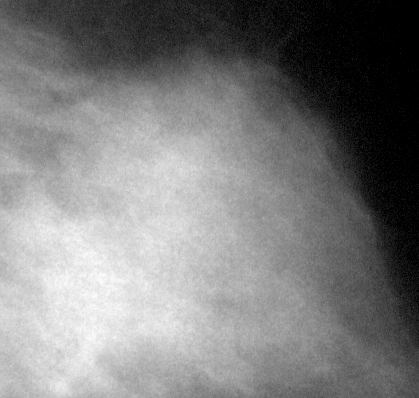
Region of interest cut from a scanned film mammogram (one marked finding), right breast, MLO view, BI-RADS breast density category 3 (scale 1–4).
Mass, shape irregular, margins ill defined; BI-RADS assessment category 4; subtlety rating 4 on a 1 (subtle) to 5 (obvious) scale; pathology (as recorded): malignant.